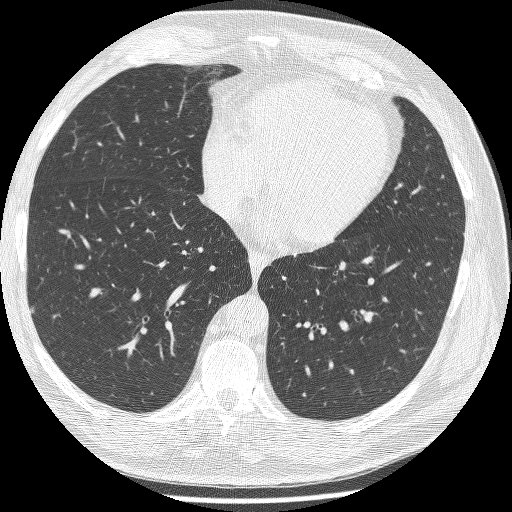
Low-dose screening chest CT, one axial slice; slice 91 of 241 in the series (ordered by position); reconstruction kernel BONE; 120 kVp; lung window (W 1500 / L -600 HU); 1.25 mm slice thickness; 512 × 512 image matrix, field of view 346 × 346 mm.
Structures marked on this image (manually delineated by an expert):
- lesion 2 (tumor, lower lobe of right lung): box from (x=30, y=306) to (x=34, y=313) px